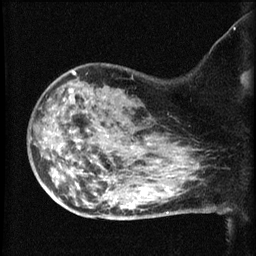
Breast MRI (dynamic contrast-enhanced), one sagittal slice. Position 44 of 60 along the scan axis. Dynamic contrast-enhanced series, image 2 of 3 at this slice position (ordered by acquisition). 1.5 T. TE 4.2 ms, TR 8.2 ms. 256 × 256 image matrix, field of view 180 × 180 mm. Patient: female, 50 years.
Outlined on this slice (semi-automatic segmentation, software-assisted and operator-edited):
- analysis volume of interest (the breast-tissue region the enhancement analysis was run in; not a lesion): box from (x=38, y=76) to (x=169, y=211) px
- tumour enhancement mask (voxels above the 70 % enhancement threshold inside the analysis volume of interest): (x=121, y=206)–(x=124, y=209)